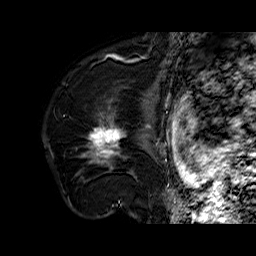
Breast MRI (dynamic contrast-enhanced), one sagittal slice; position 45 of 60 along the scan axis; dynamic contrast-enhanced series, time point 2 of 6 at this slice position (early post-contrast); 1.5 T; TE 6.4 ms, TR 32.7 ms; 256 × 256 image matrix. Female patient. From the clinical record (not read from this slice): setting: breast cancer imaged before/during neoadjuvant chemotherapy; receptor status: HR-positive, HER2-negative.
Structures marked on this image (semi-automatic segmentation, software-assisted and operator-edited):
- analysis volume of interest (the breast-tissue region the enhancement analysis was run in; not a lesion): bounding box [x1, y1, x2, y2] px = [76, 110, 141, 178]
- tumour enhancement mask (voxels above the 100 % enhancement threshold inside the analysis volume of interest): [89, 120, 121, 163]